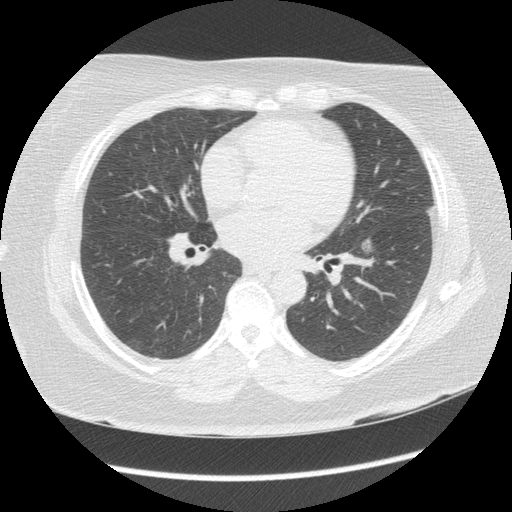
Low-dose screening chest CT, axial slice; third screening round (two years after baseline); lung window (W 1500 / L -600 HU); 2.5 mm slice thickness; 512 × 512 image matrix. Female, age 65 years at enrolment.
• Lesion marked by an expert reader, bounding box <350,231,379,266> (left, top, right, bottom; pixels).
• The exam's reader record, not a measurement of the box and not confirmed to be the same lesion: non-calcified nodule or mass ≥4 mm, left lower lobe, 130 × 90 mm, poorly defined margins, mixed attenuation, pre-existing on the prior screen: yes; interval growth: yes.
• Official screen result: positive, other.
• Lung cancer was diagnosed 35 days after this screen: adenocarcinoma, NOS, left lower lobe, moderately differentiated (G2), stage IA (AJCC 6th edition), 12 mm at pathology.